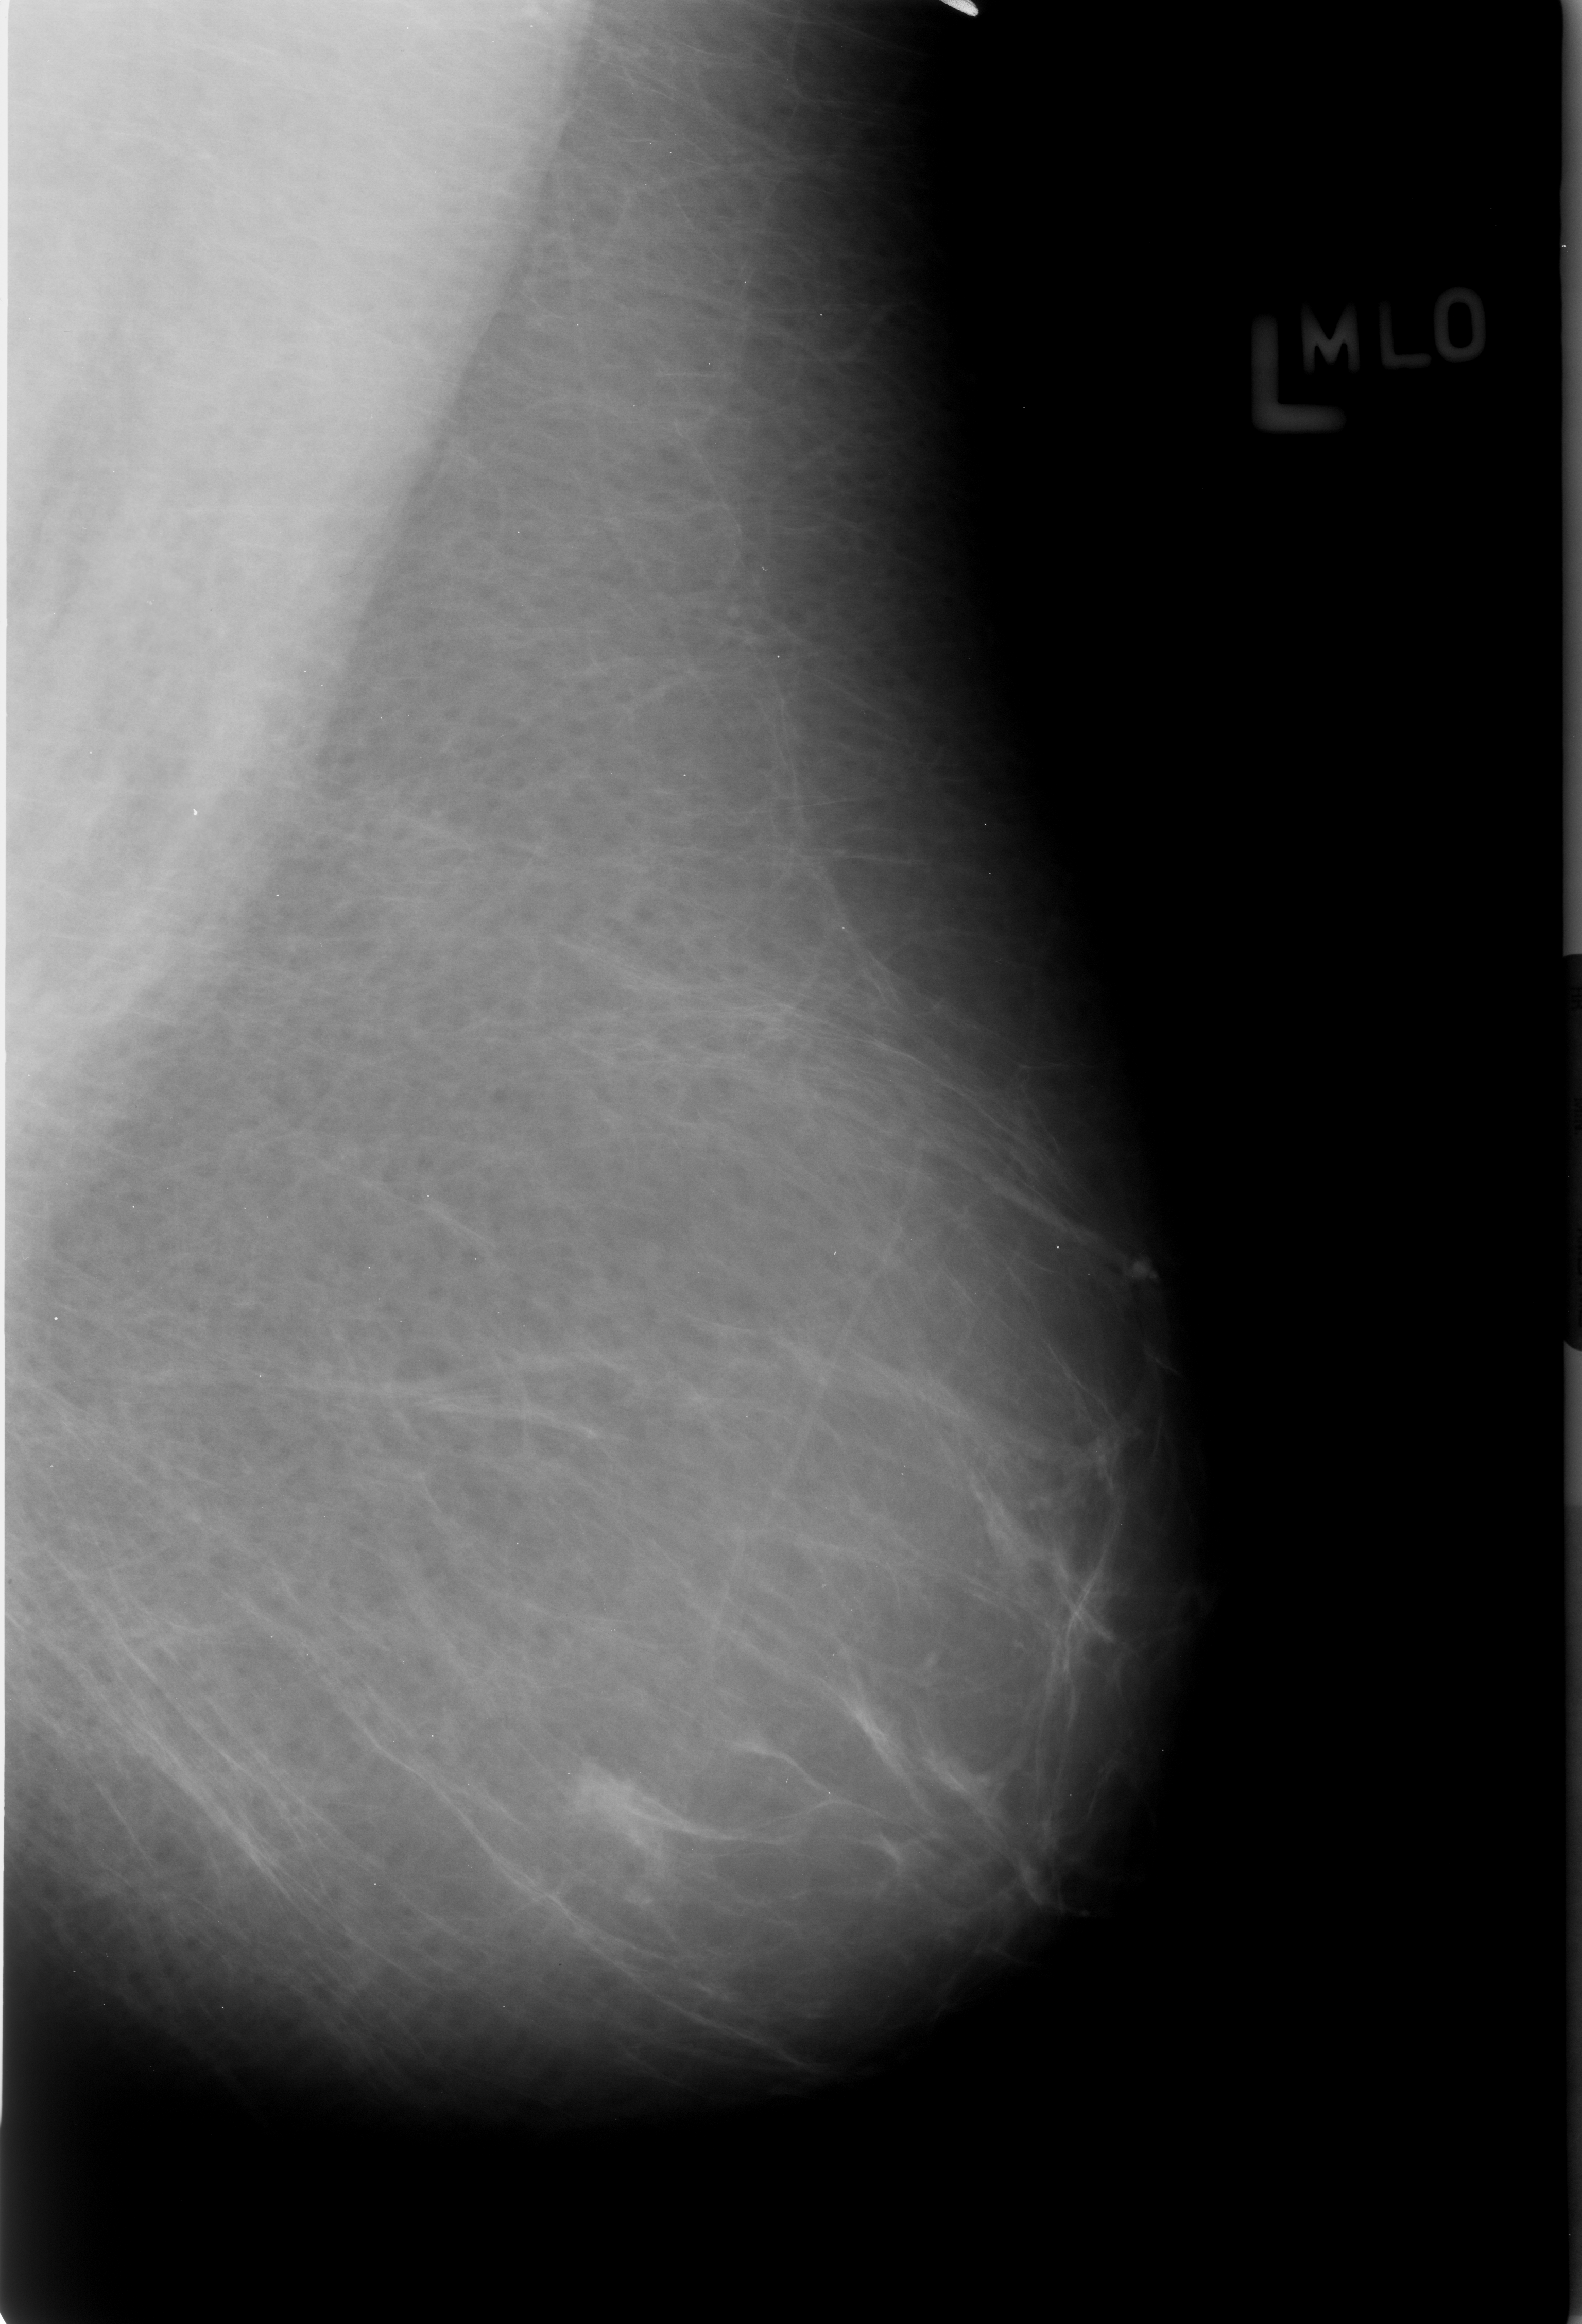
Digitized screen-film mammogram; left breast; MLO view; breast composition: almost entirely fatty (BI-RADS density category 1 of 4).
- Mass, shape irregular, margins ill defined; BI-RADS assessment category 4; subtlety rating 4 on a 1 (subtle) to 5 (obvious) scale; pathology result (as recorded, not read from the image): benign.